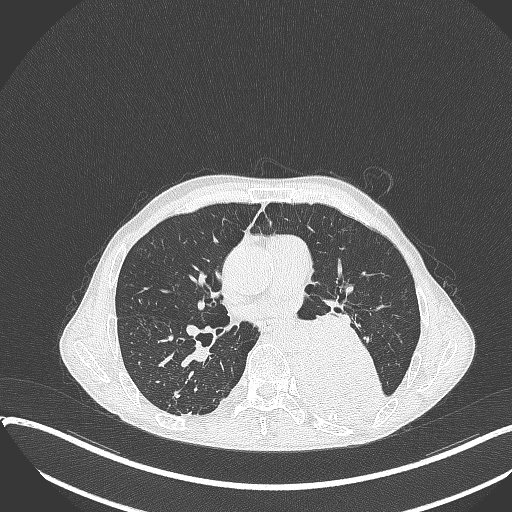
Chest CT, one axial slice; slice 193 of 401 in the series (ordered by position); reconstruction kernel B70f; lung window (W 1500 / L -600 HU); 1 mm slice thickness; 512 × 512 image matrix. Patient: male, 57 years. Case-level facts recorded for this patient, not image findings: clinical TNM (as recorded): T4 N0 M0.
Annotated regions visible in this slice (rectangle marked by the reading radiologist):
- lung tumour (recorded histology: squamous cell carcinoma): bounding box <289,330,383,418> (left, top, right, bottom; pixels)